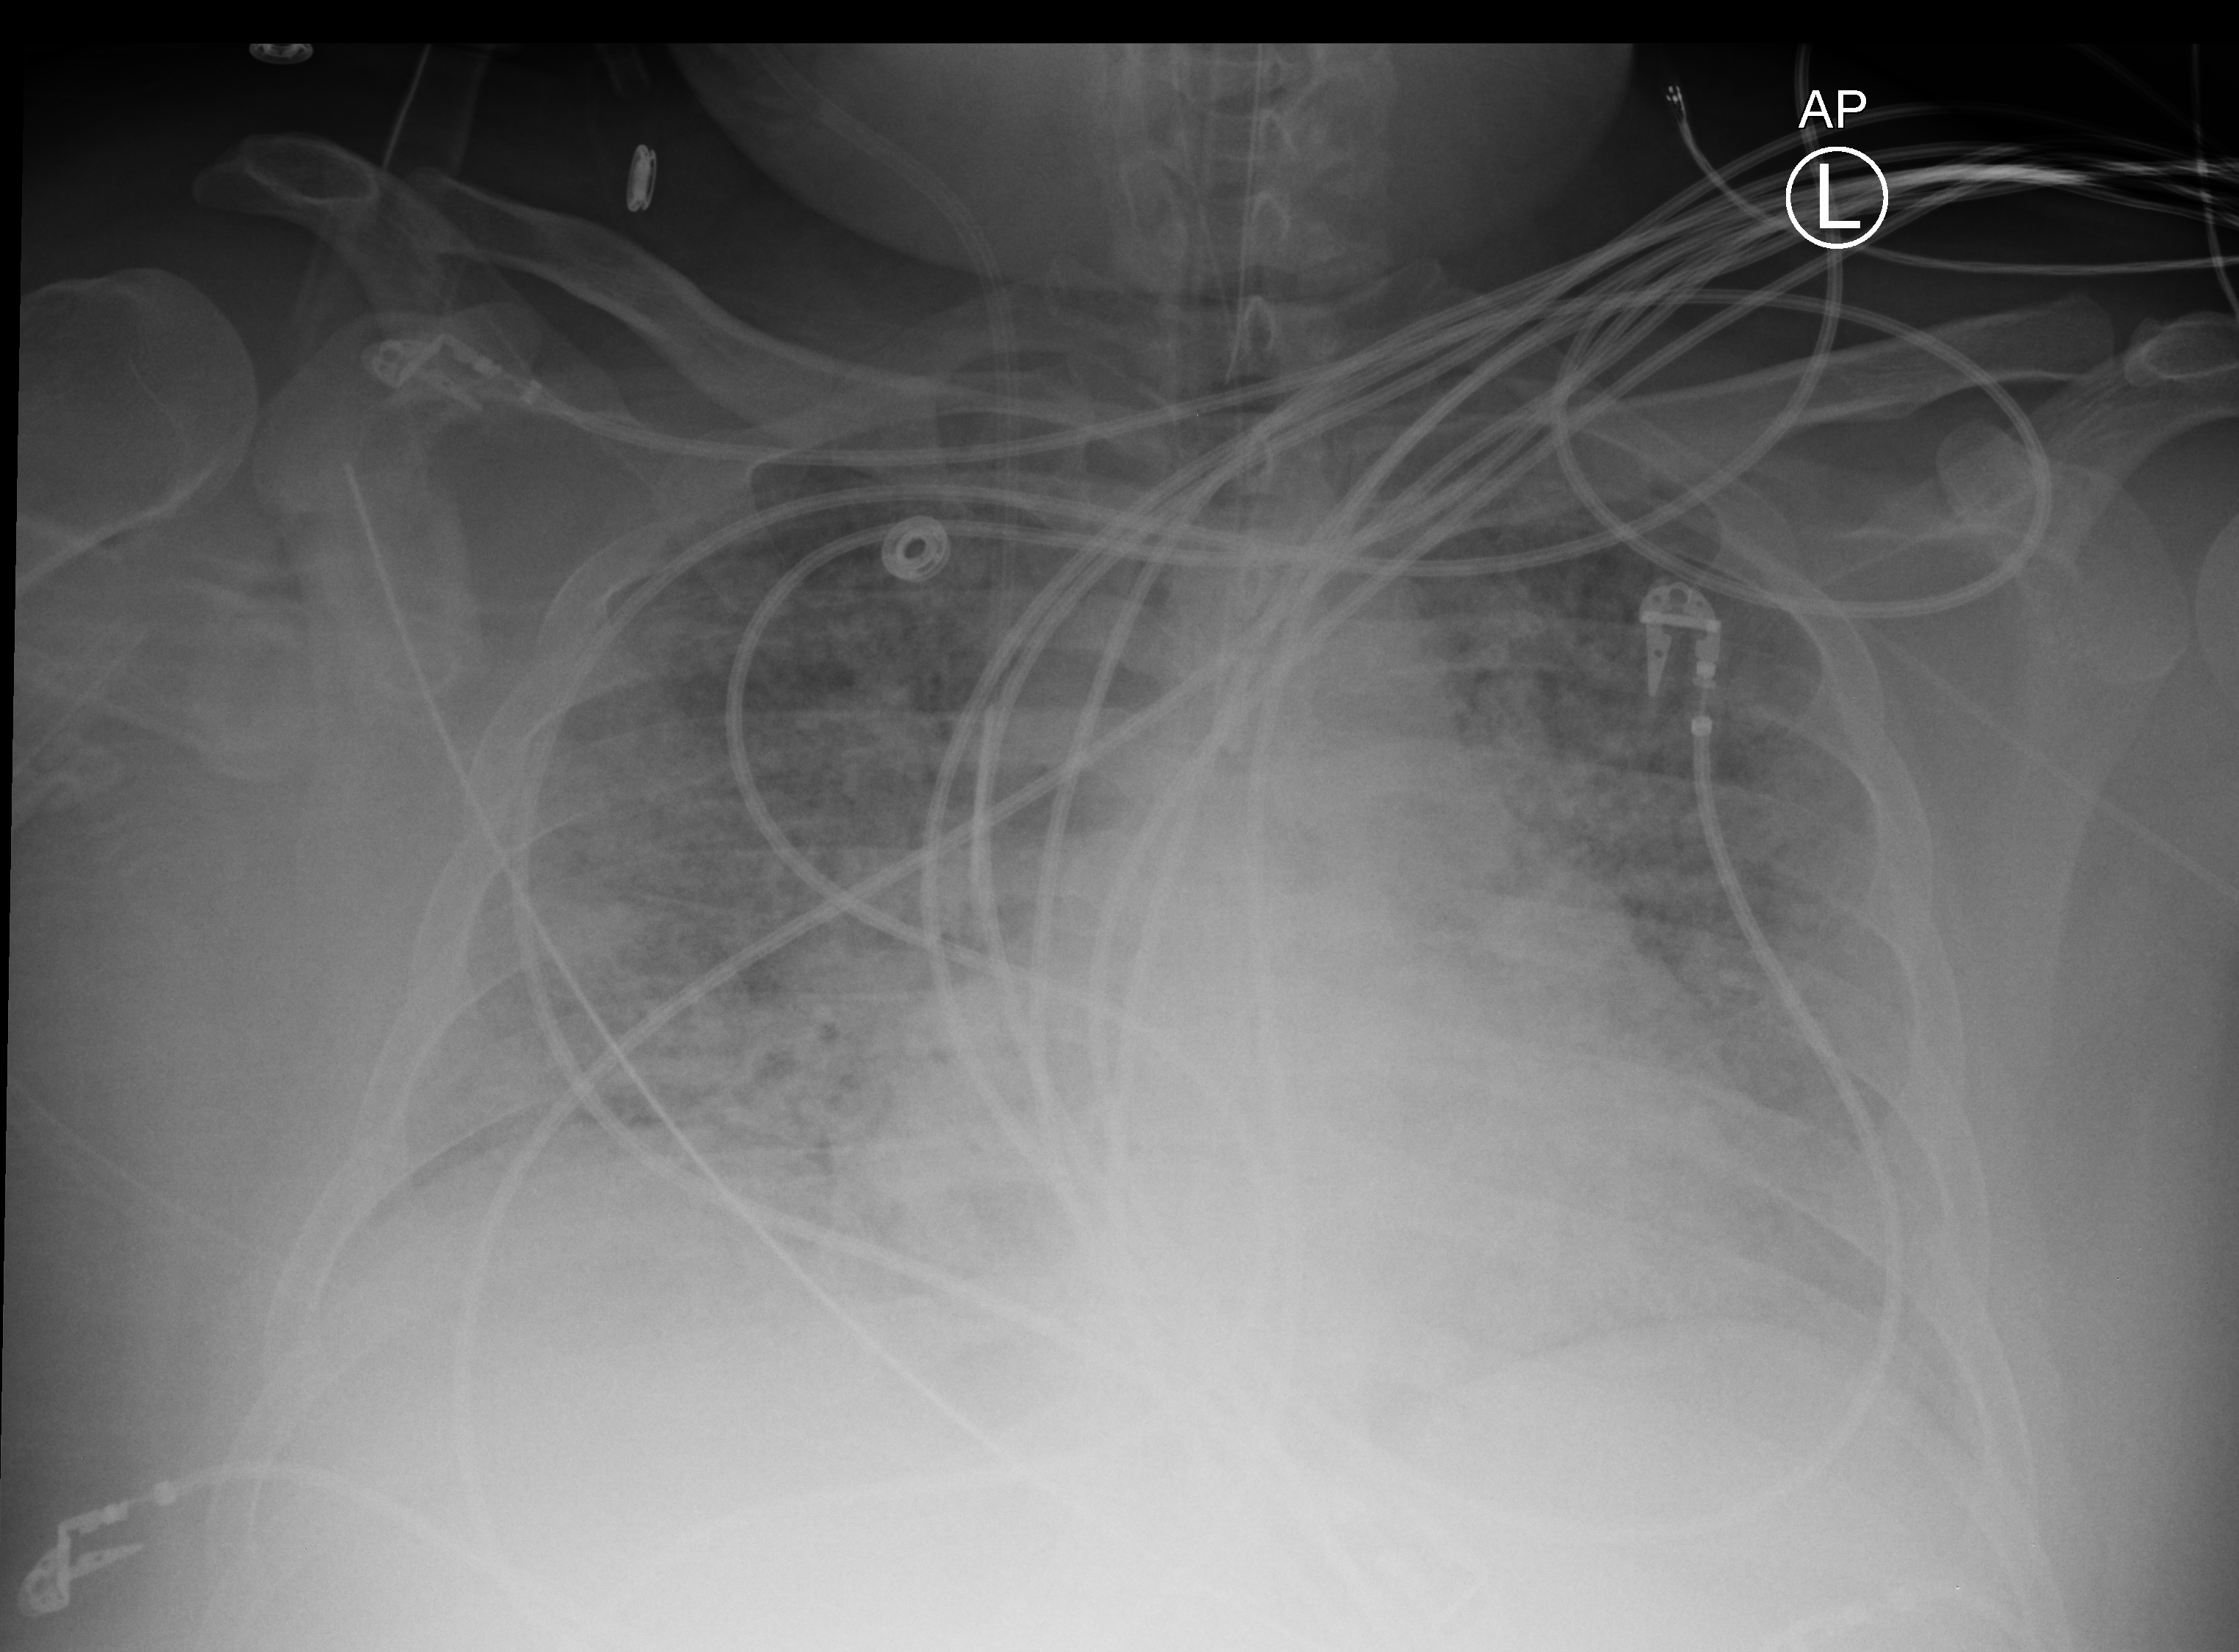
Bedside chest radiograph (computed radiography). Adult patient hospitalised with COVID-19, age 18–59 years.
Admission-level facts for this patient (not findings on this image; timing relative to this image not recorded): chronic kidney disease (admission record): no; diabetes (admission record): no.